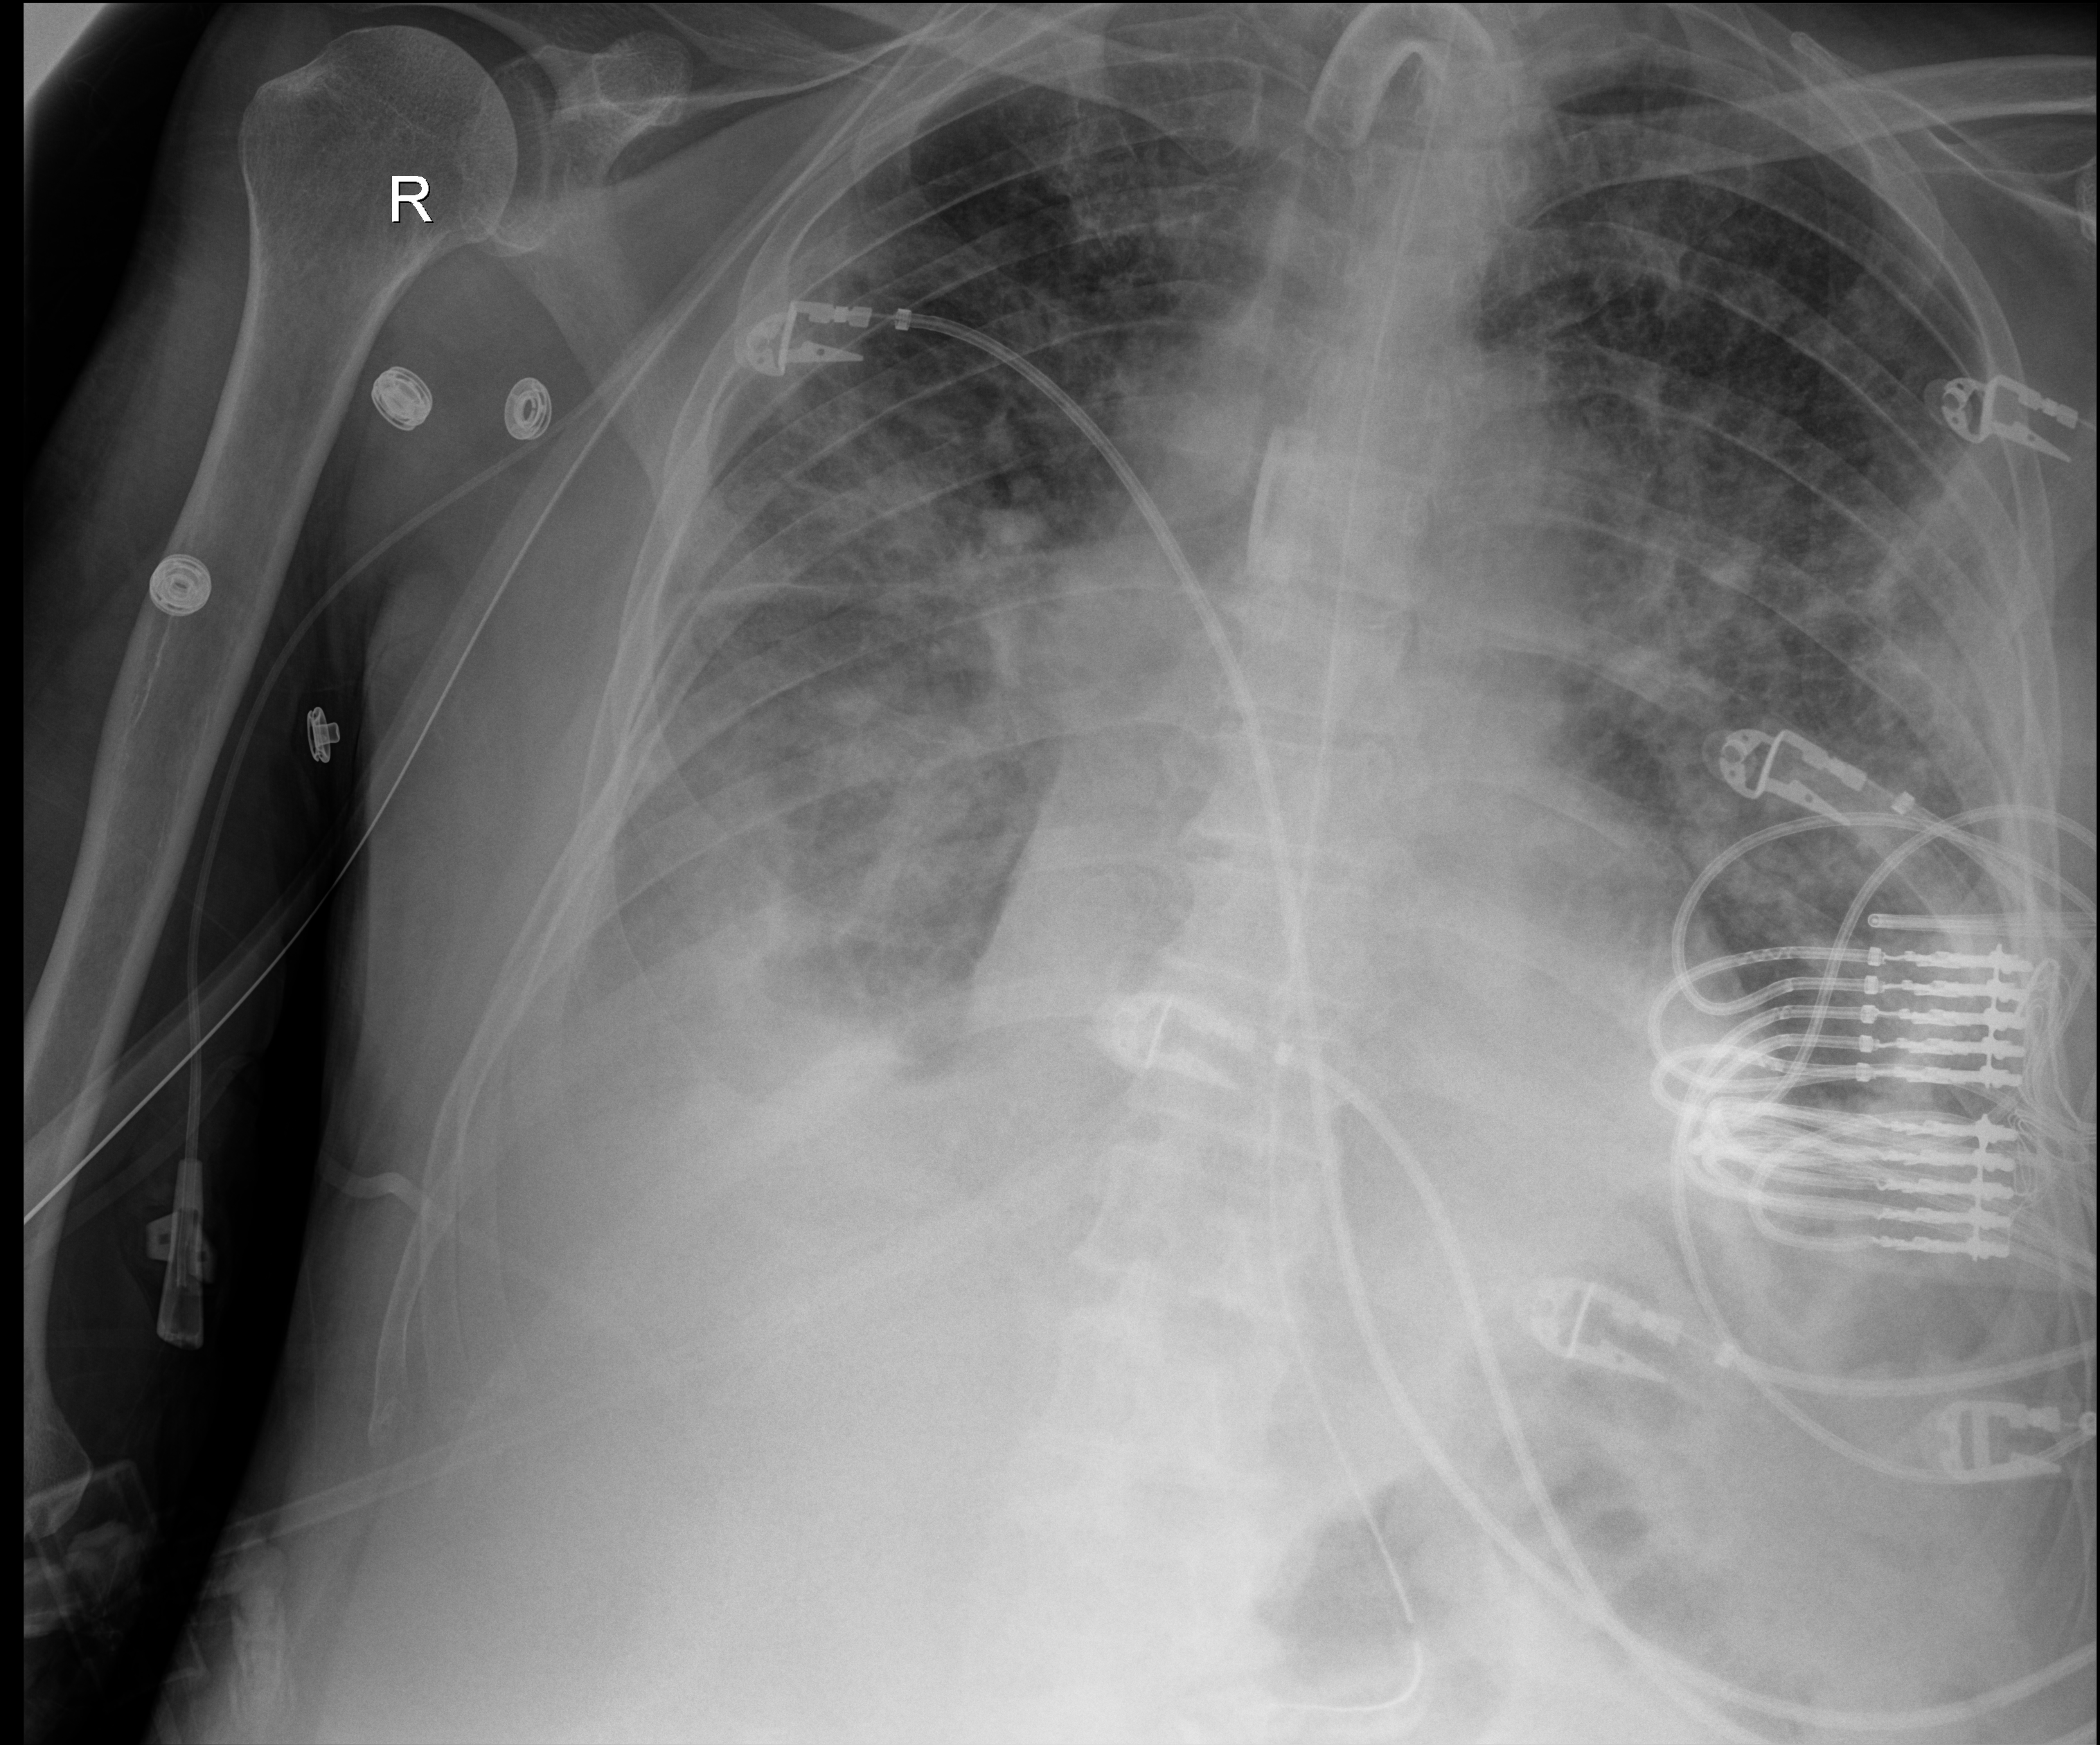
Chest X-ray (portable). Patient hospitalised with COVID-19; male, aged 75–90 years.
Admission-level facts for this patient (not findings on this image; timing relative to this image not recorded):
- mechanically ventilated during this hospital stay: yes
- admitted to intensive care during this hospital stay: yes